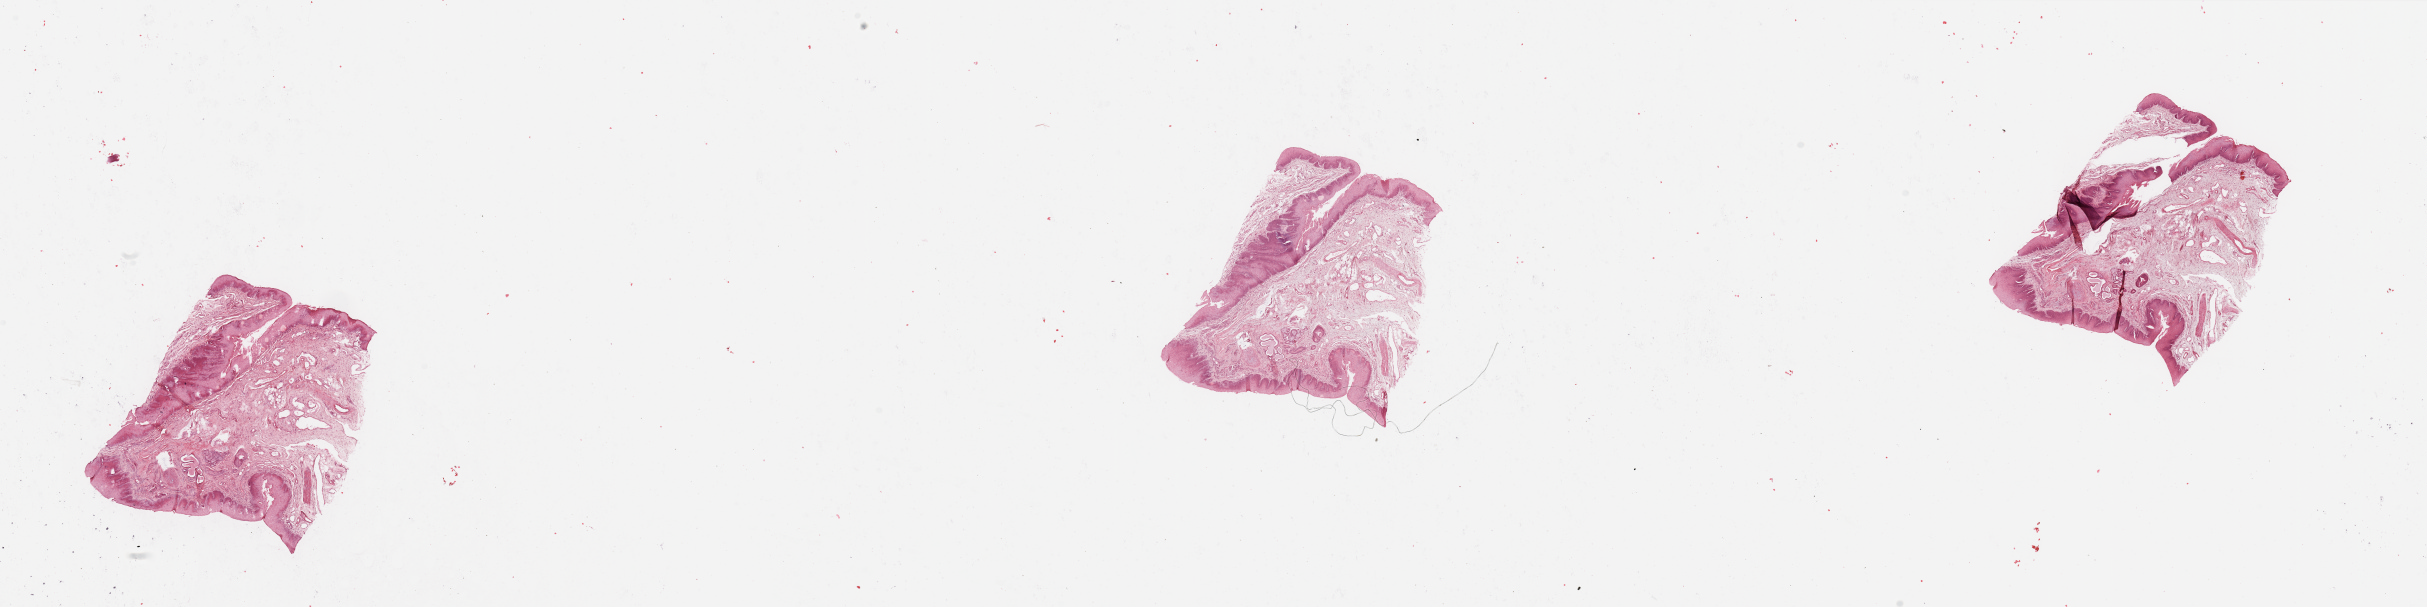
H&E-stained whole-slide image — whole scanned area (about 38.4 x 9.6 mm) shown as a low-resolution overview. Head and neck, normal (non-tumour) tissue. Male, 71 y/o.
This section: normal (non-tumour) tissue from the same patient. Patient diagnosis: Squamous cell carcinoma, NOS (larynx, NOS).